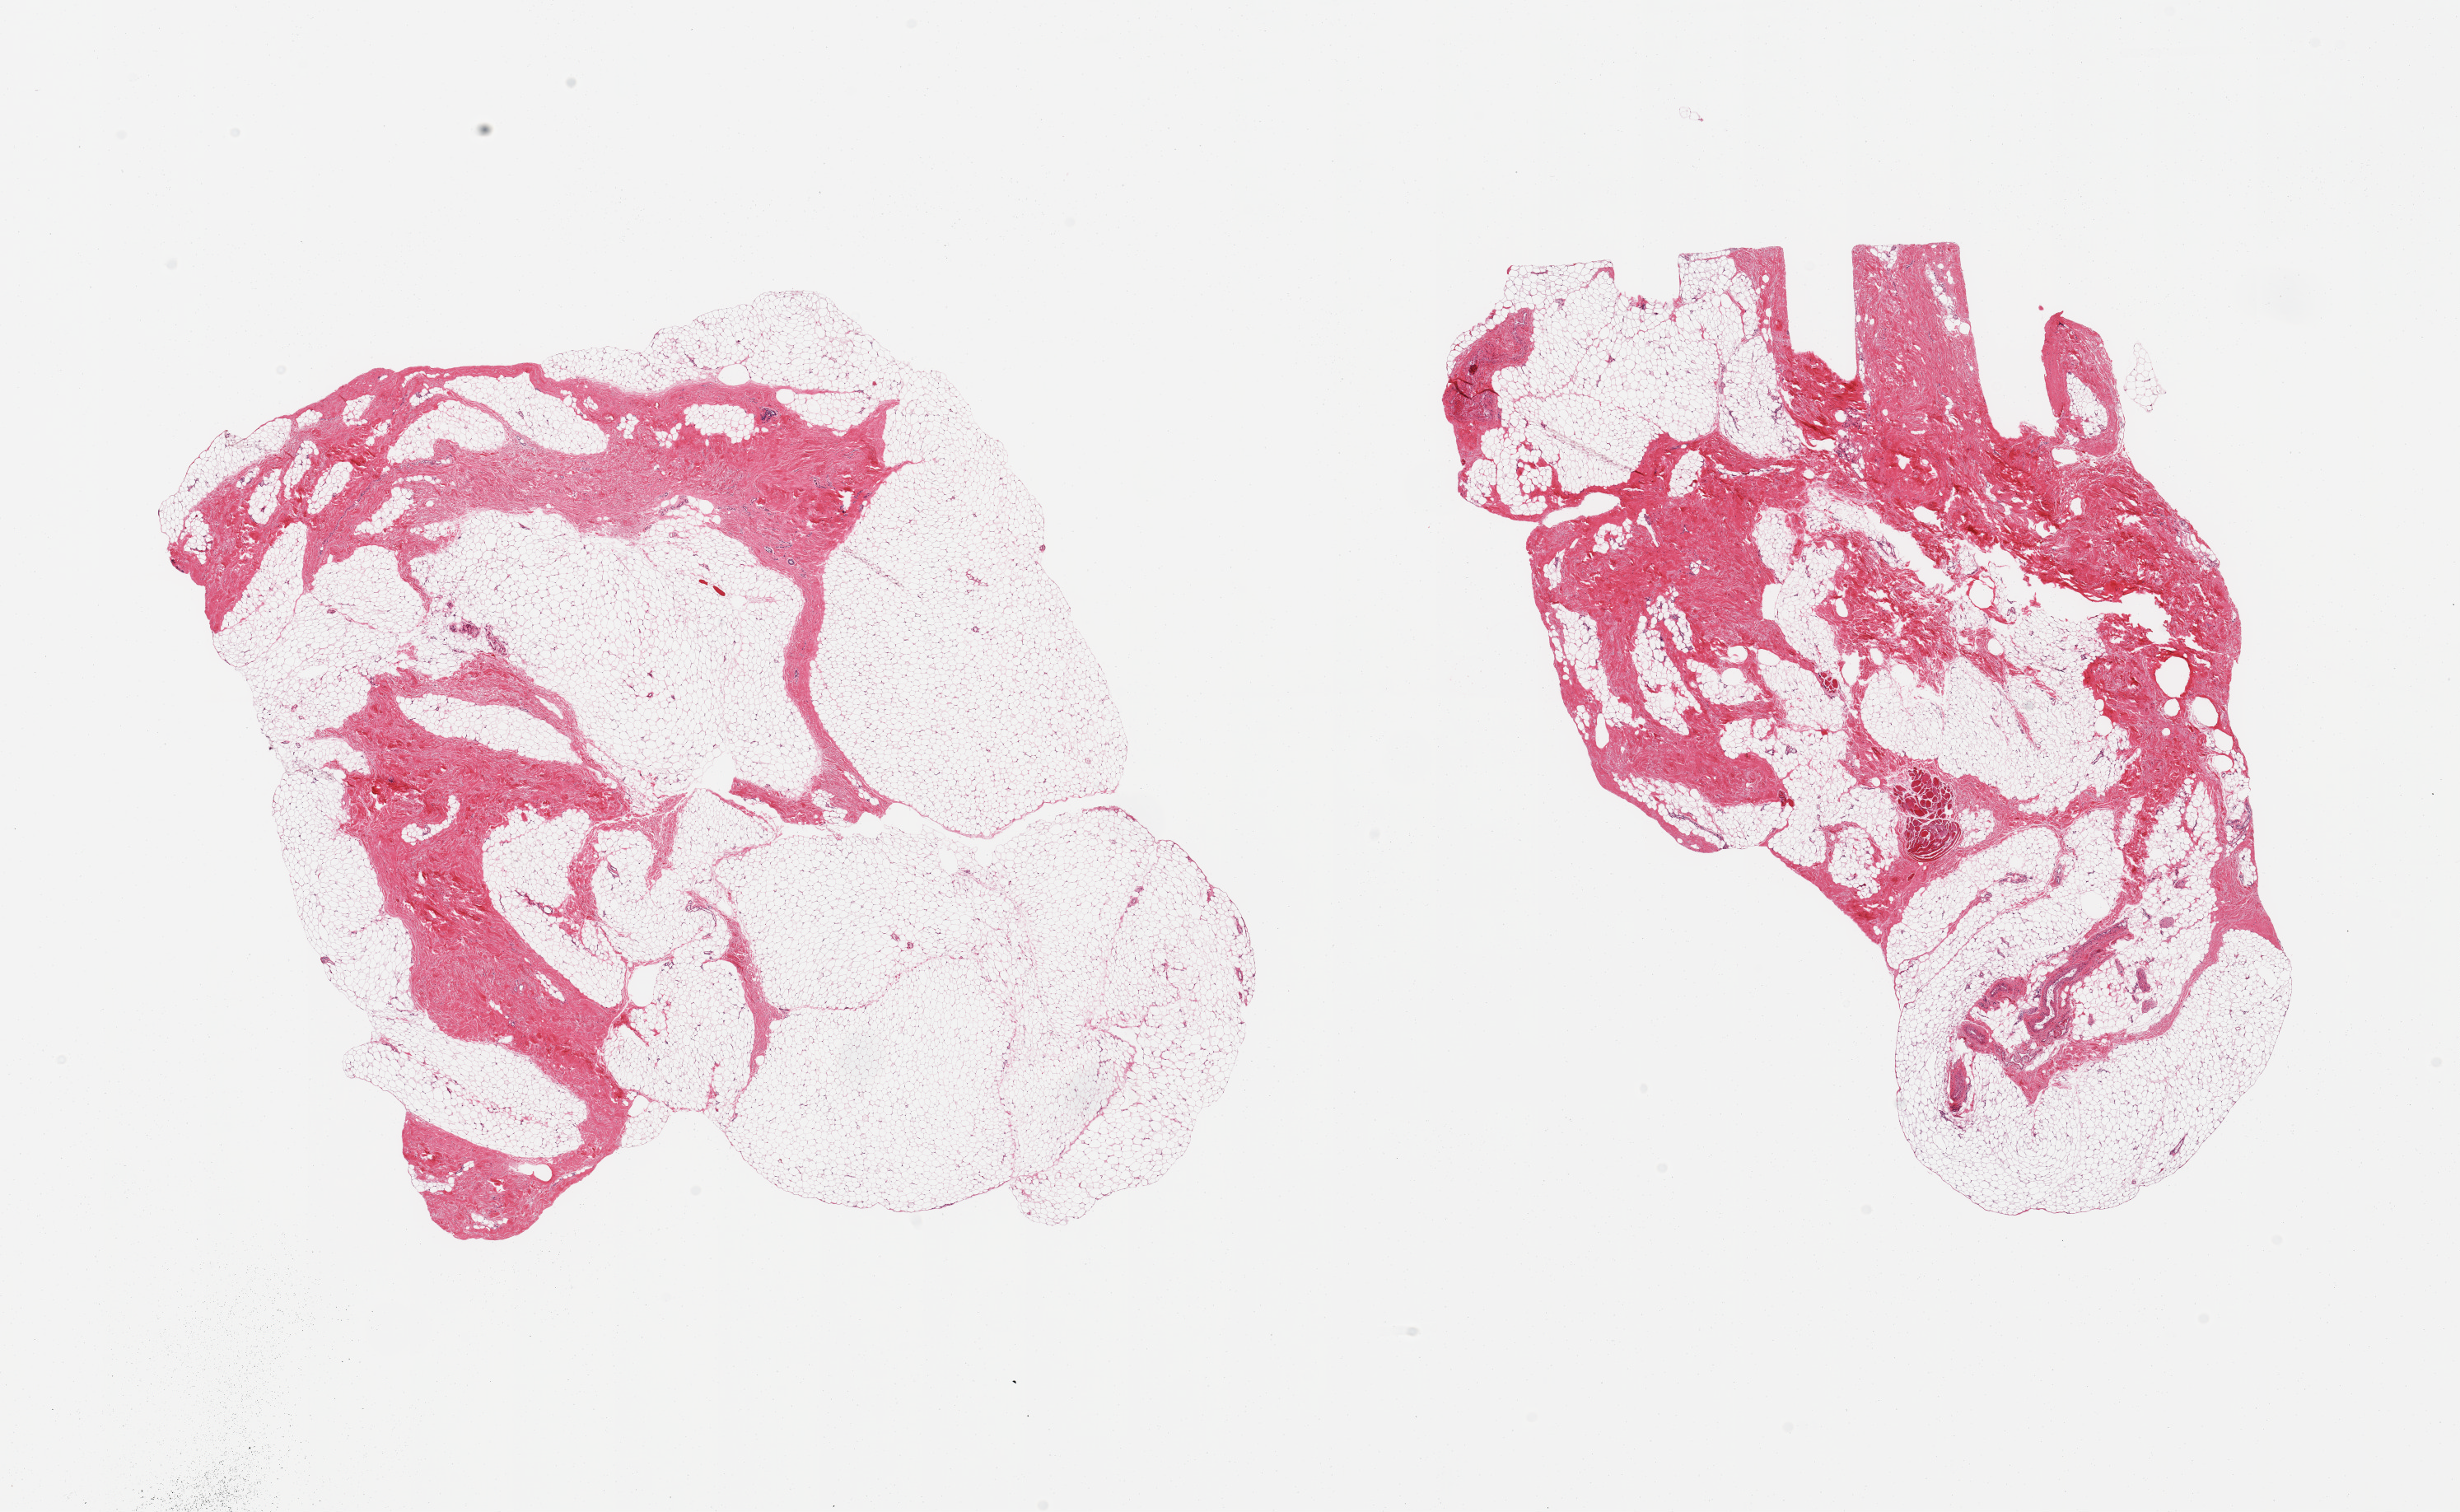
Digitized H&E-stained section, a low-resolution overview of the entire scanned area, about 23.6 x 14.5 mm, PAXgene-fixed, paraffin-embedded tissue, section of breast (target tissue), donor tissue sample. Donor sex: male.
Review note (as recorded): 2 pieces fibroadipose elements, gynecomastoid stromal hyerplasia; trace ductal elements.